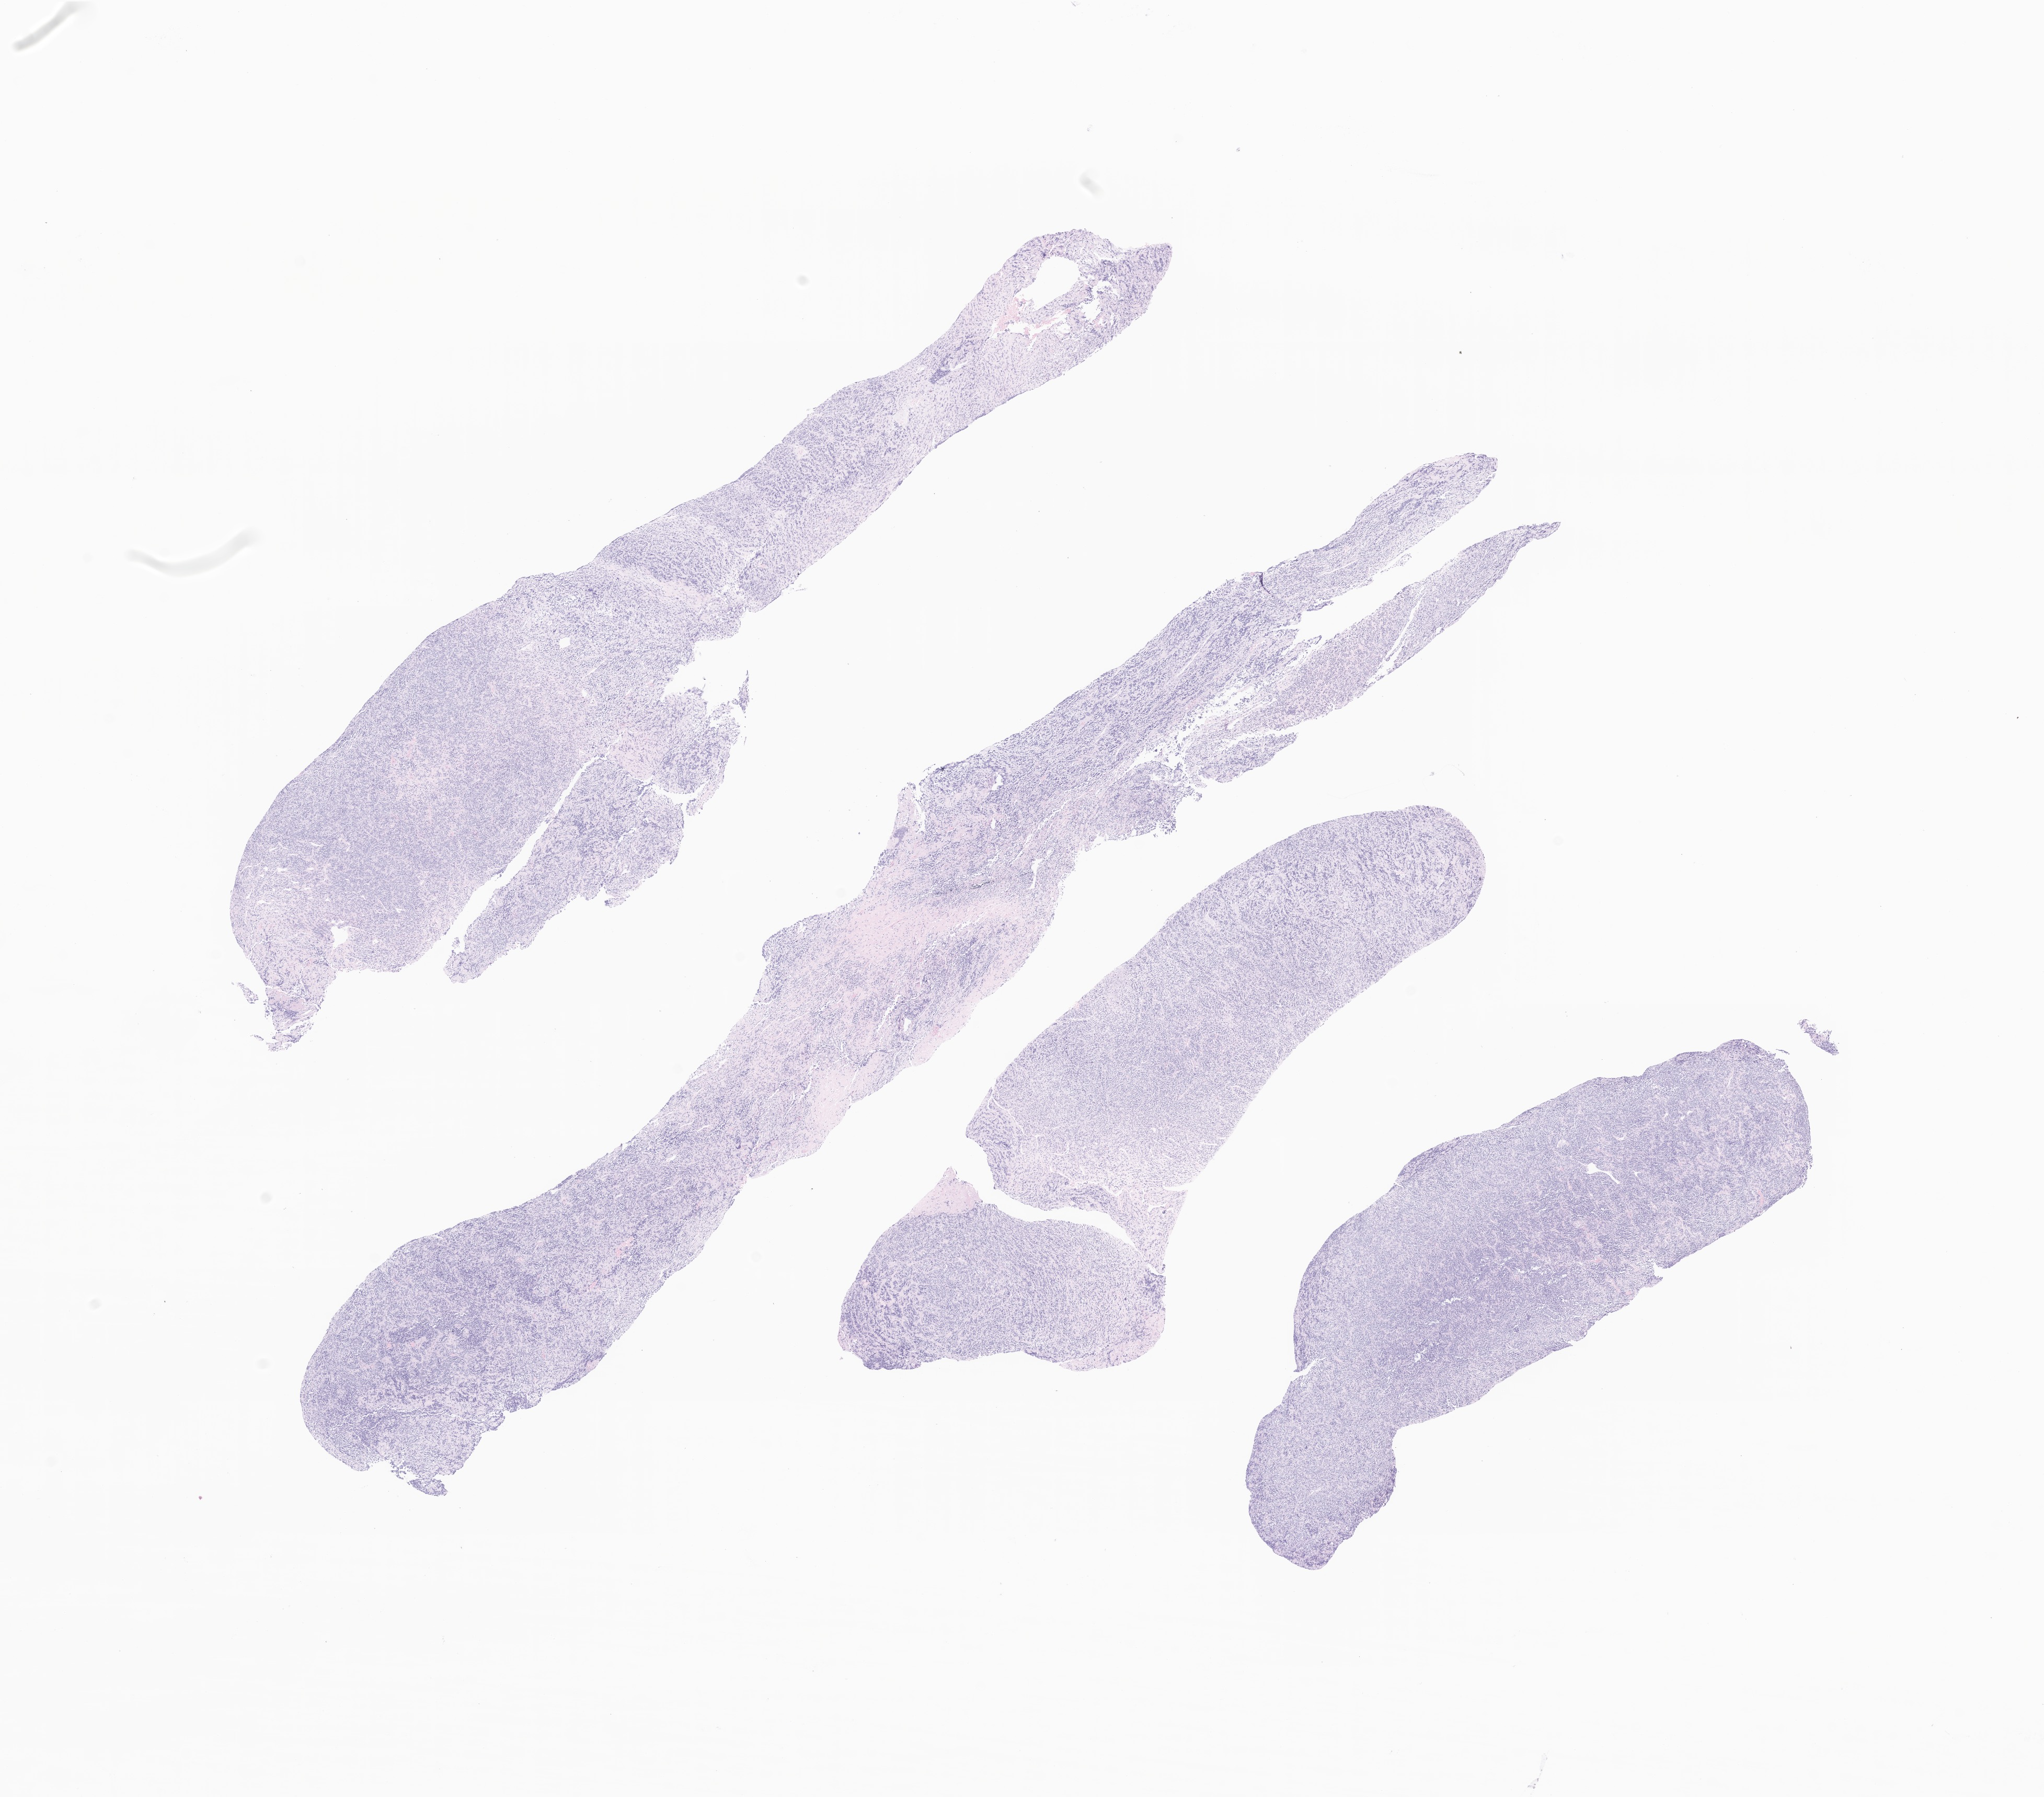
Digitized H&E-stained section of tumor tissue from the head and neck — shown as a low-resolution overview of the whole scanned area (about 16.5 x 14.5 mm); FFPE section. Patient male; age 62 months (5 years 2 months).
Diagnosis: Rhabdomyosarcoma, NOS.